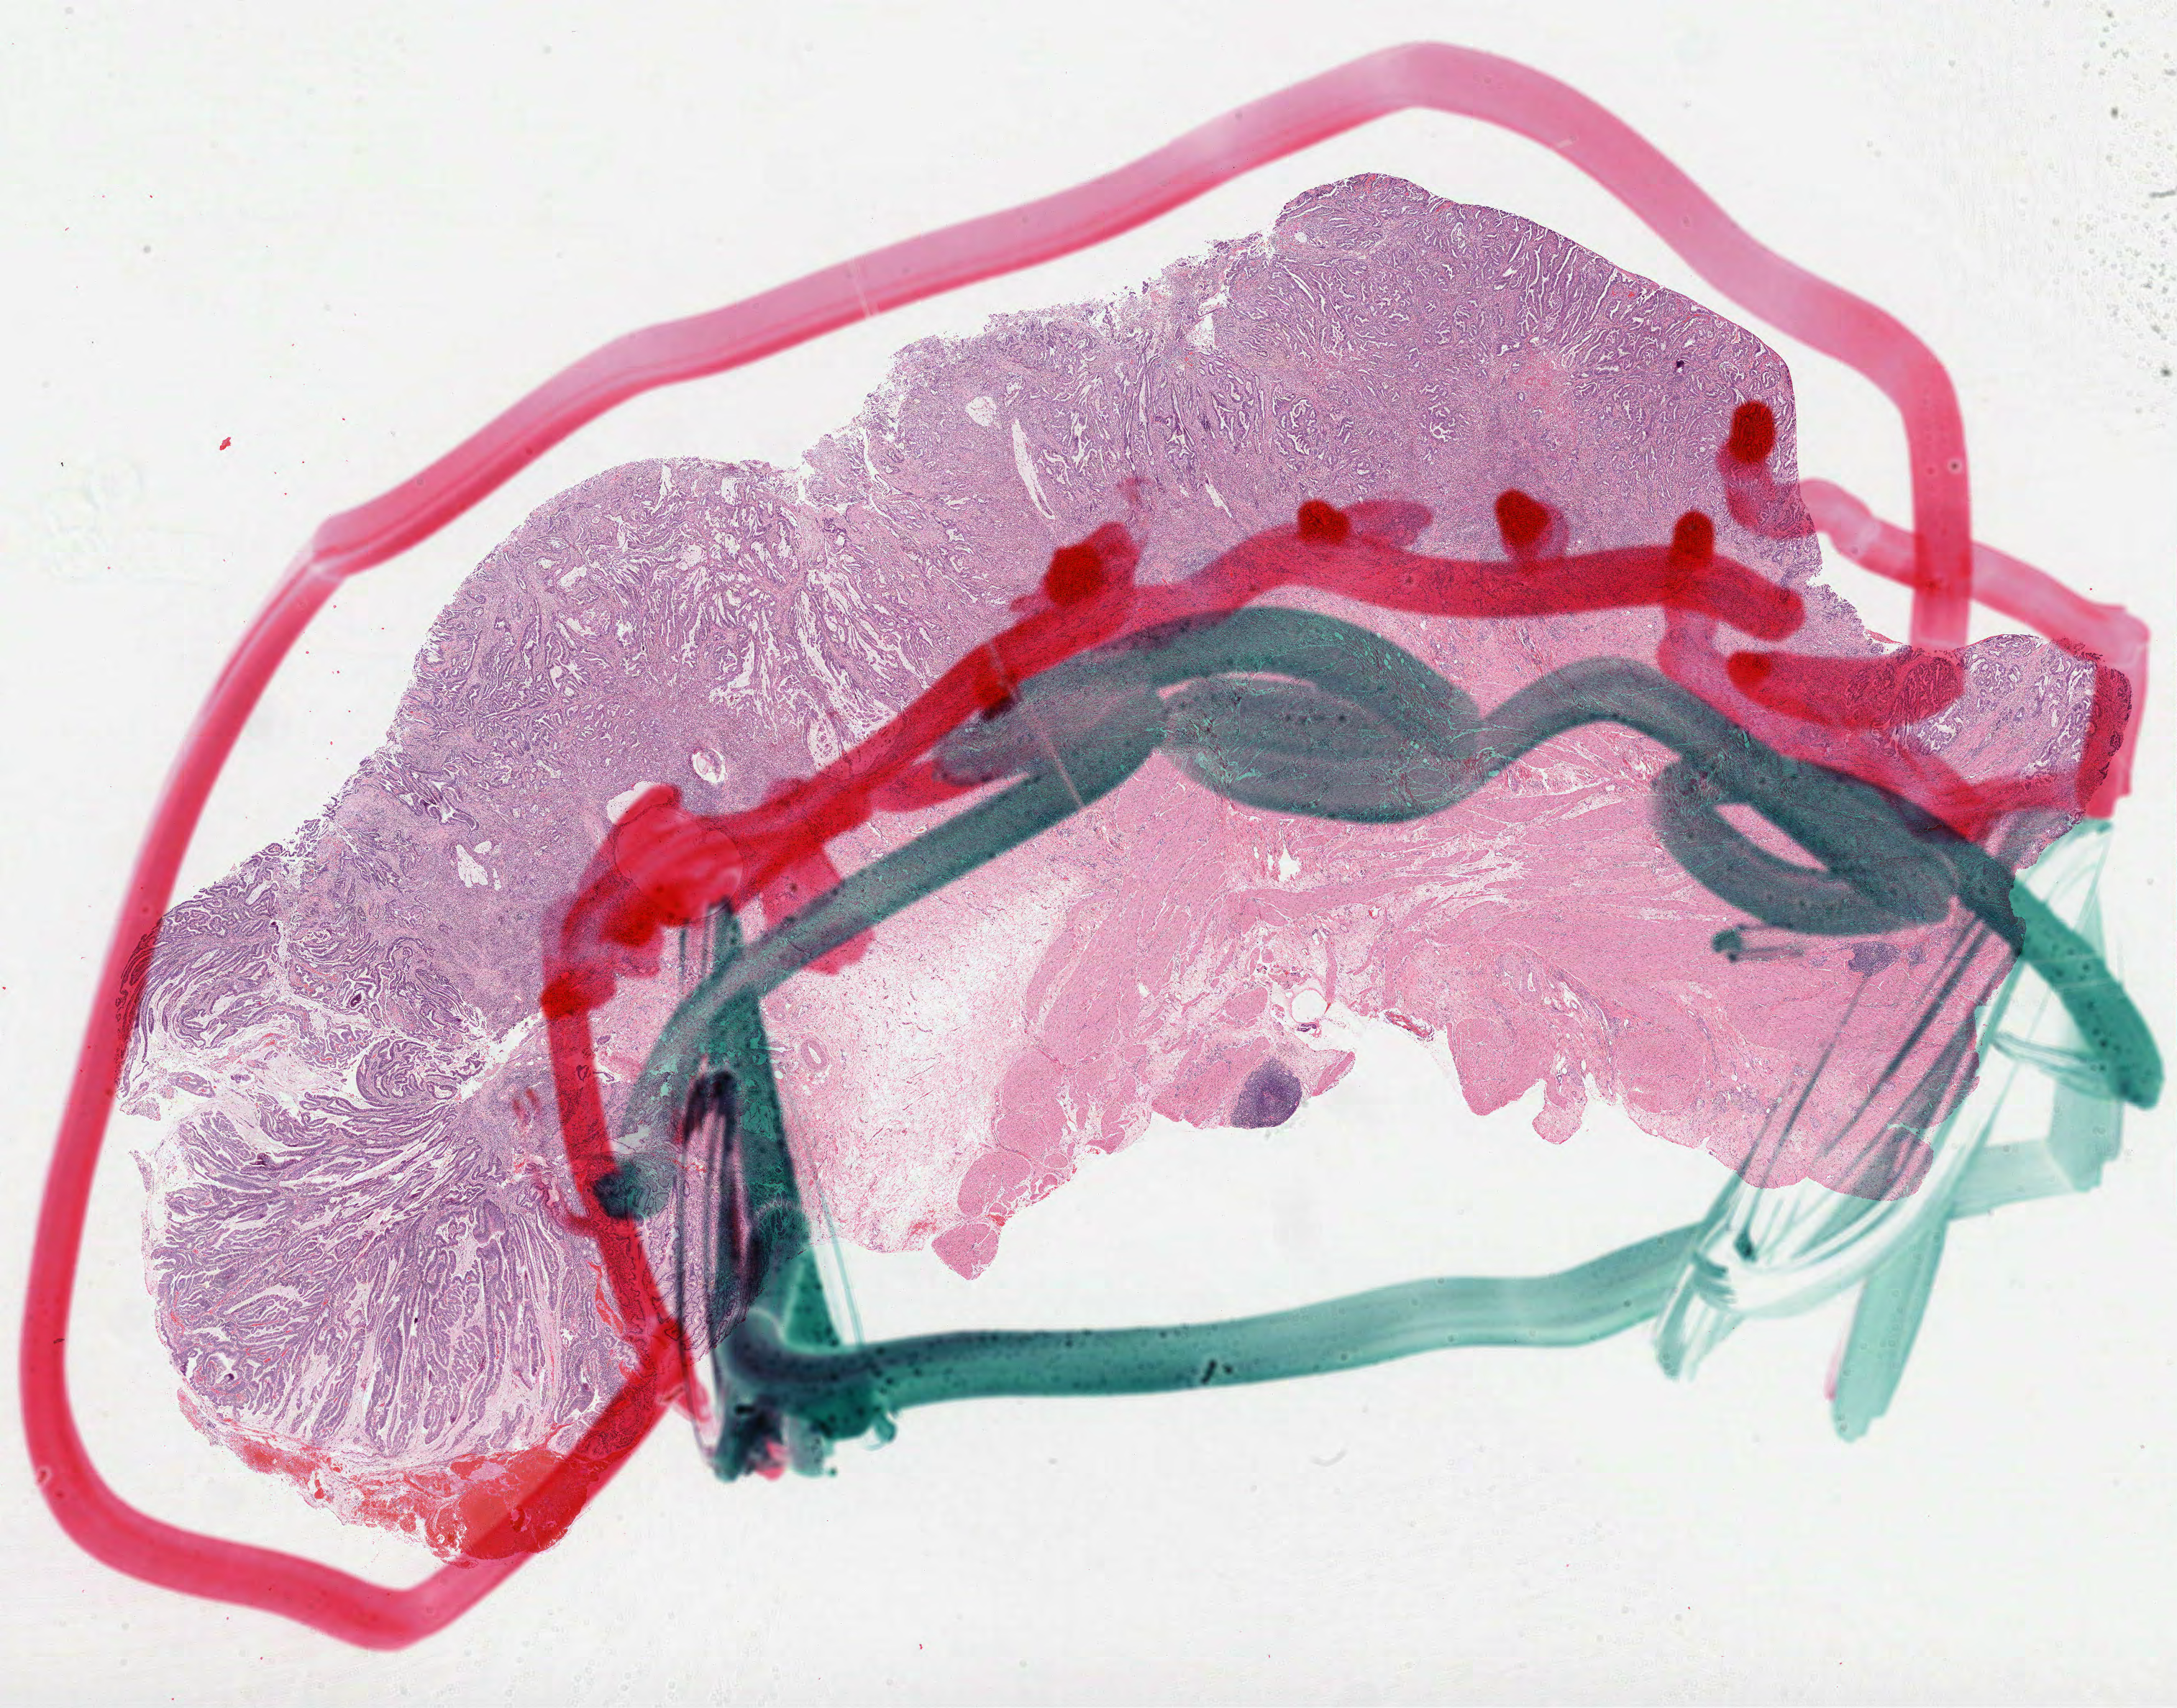
H&E-stained whole-slide image, whole scanned area (about 24.4 x 19.2 mm, from a 40x scan) shown as a low-resolution overview, FFPE section, primary tumour sample from the stomach. Patient: female, age at initial diagnosis 69 years. Histologic grade: G3 (poorly differentiated).
* lymph nodes positive (case pathology): 0 of 2 examined
* AJCC pathologic stage: IB (7th edition)
* pathologic diagnosis: Adenocarcinoma, NOS (body of stomach)